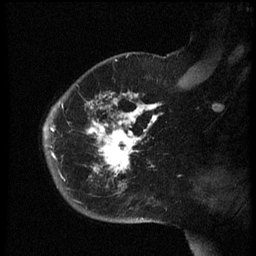
Breast MRI (dynamic contrast-enhanced), one sagittal slice; position 44 of 60 along the scan axis; dynamic contrast-enhanced series, image 2 of 3 at this slice position (ordered by acquisition); 1.5 T; TE 4.2 ms, TR 8.4 ms; 2.5 mm slice thickness; 256 × 256 image matrix. Patient: female, 38 years. From the clinical record (not read from this slice): setting: breast cancer imaged before/during neoadjuvant chemotherapy; receptor status: HER2-positive.
Outlined on this slice (semi-automatically segmented with operator editing):
- analysis volume of interest (the breast-tissue region the enhancement analysis was run in; not a lesion): bounding box <44,74,163,202> (left, top, right, bottom; pixels)
- tumour enhancement mask (voxels above the 70 % enhancement threshold inside the analysis volume of interest): <45,93,160,190>